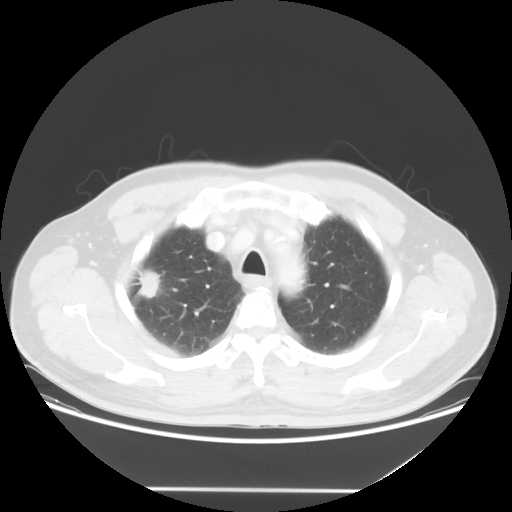
Chest CT, one axial slice; position 43 of 54 along the scan axis; reconstruction kernel STANDARD; 120 kVp; lung window (W 1500 / L -600 HU); 512 × 512 image matrix, field of view 416 × 416 mm. Patient: male, 65 years. From the clinical record (not read from this slice): clinical TNM (as recorded): T1c N1 M0.
Outlined on this slice (rectangle marked by the reading radiologist):
- lung tumour (recorded histology: adenocarcinoma): box from (x=135, y=267) to (x=163, y=302) px